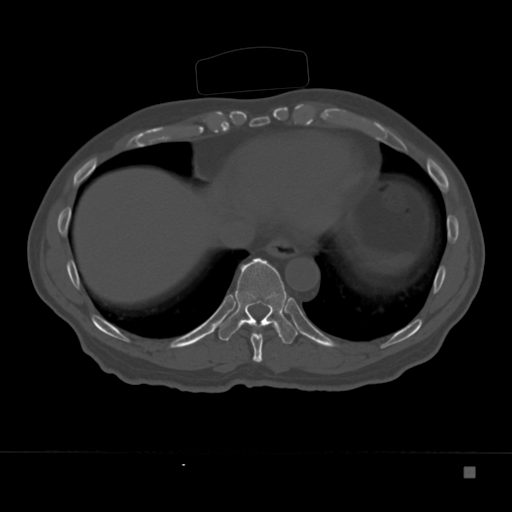
CT including the spine, one axial slice. Reconstruction kernel Br40s. Bone window (W 1800 / L 400 HU). 1.5 mm slice thickness. 512 × 512 image matrix, field of view 389 × 389 mm. Male patient, age 72 years. From the clinical record (not read from this slice): primary cancer: skeletal.
Outlined on this slice (semi-automatically segmented with operator editing):
- T10 vertebra: bounding box (x1, y1, x2, y2) in pixels: (218, 258, 298, 344)
- T9 vertebra: (238, 322, 263, 362)